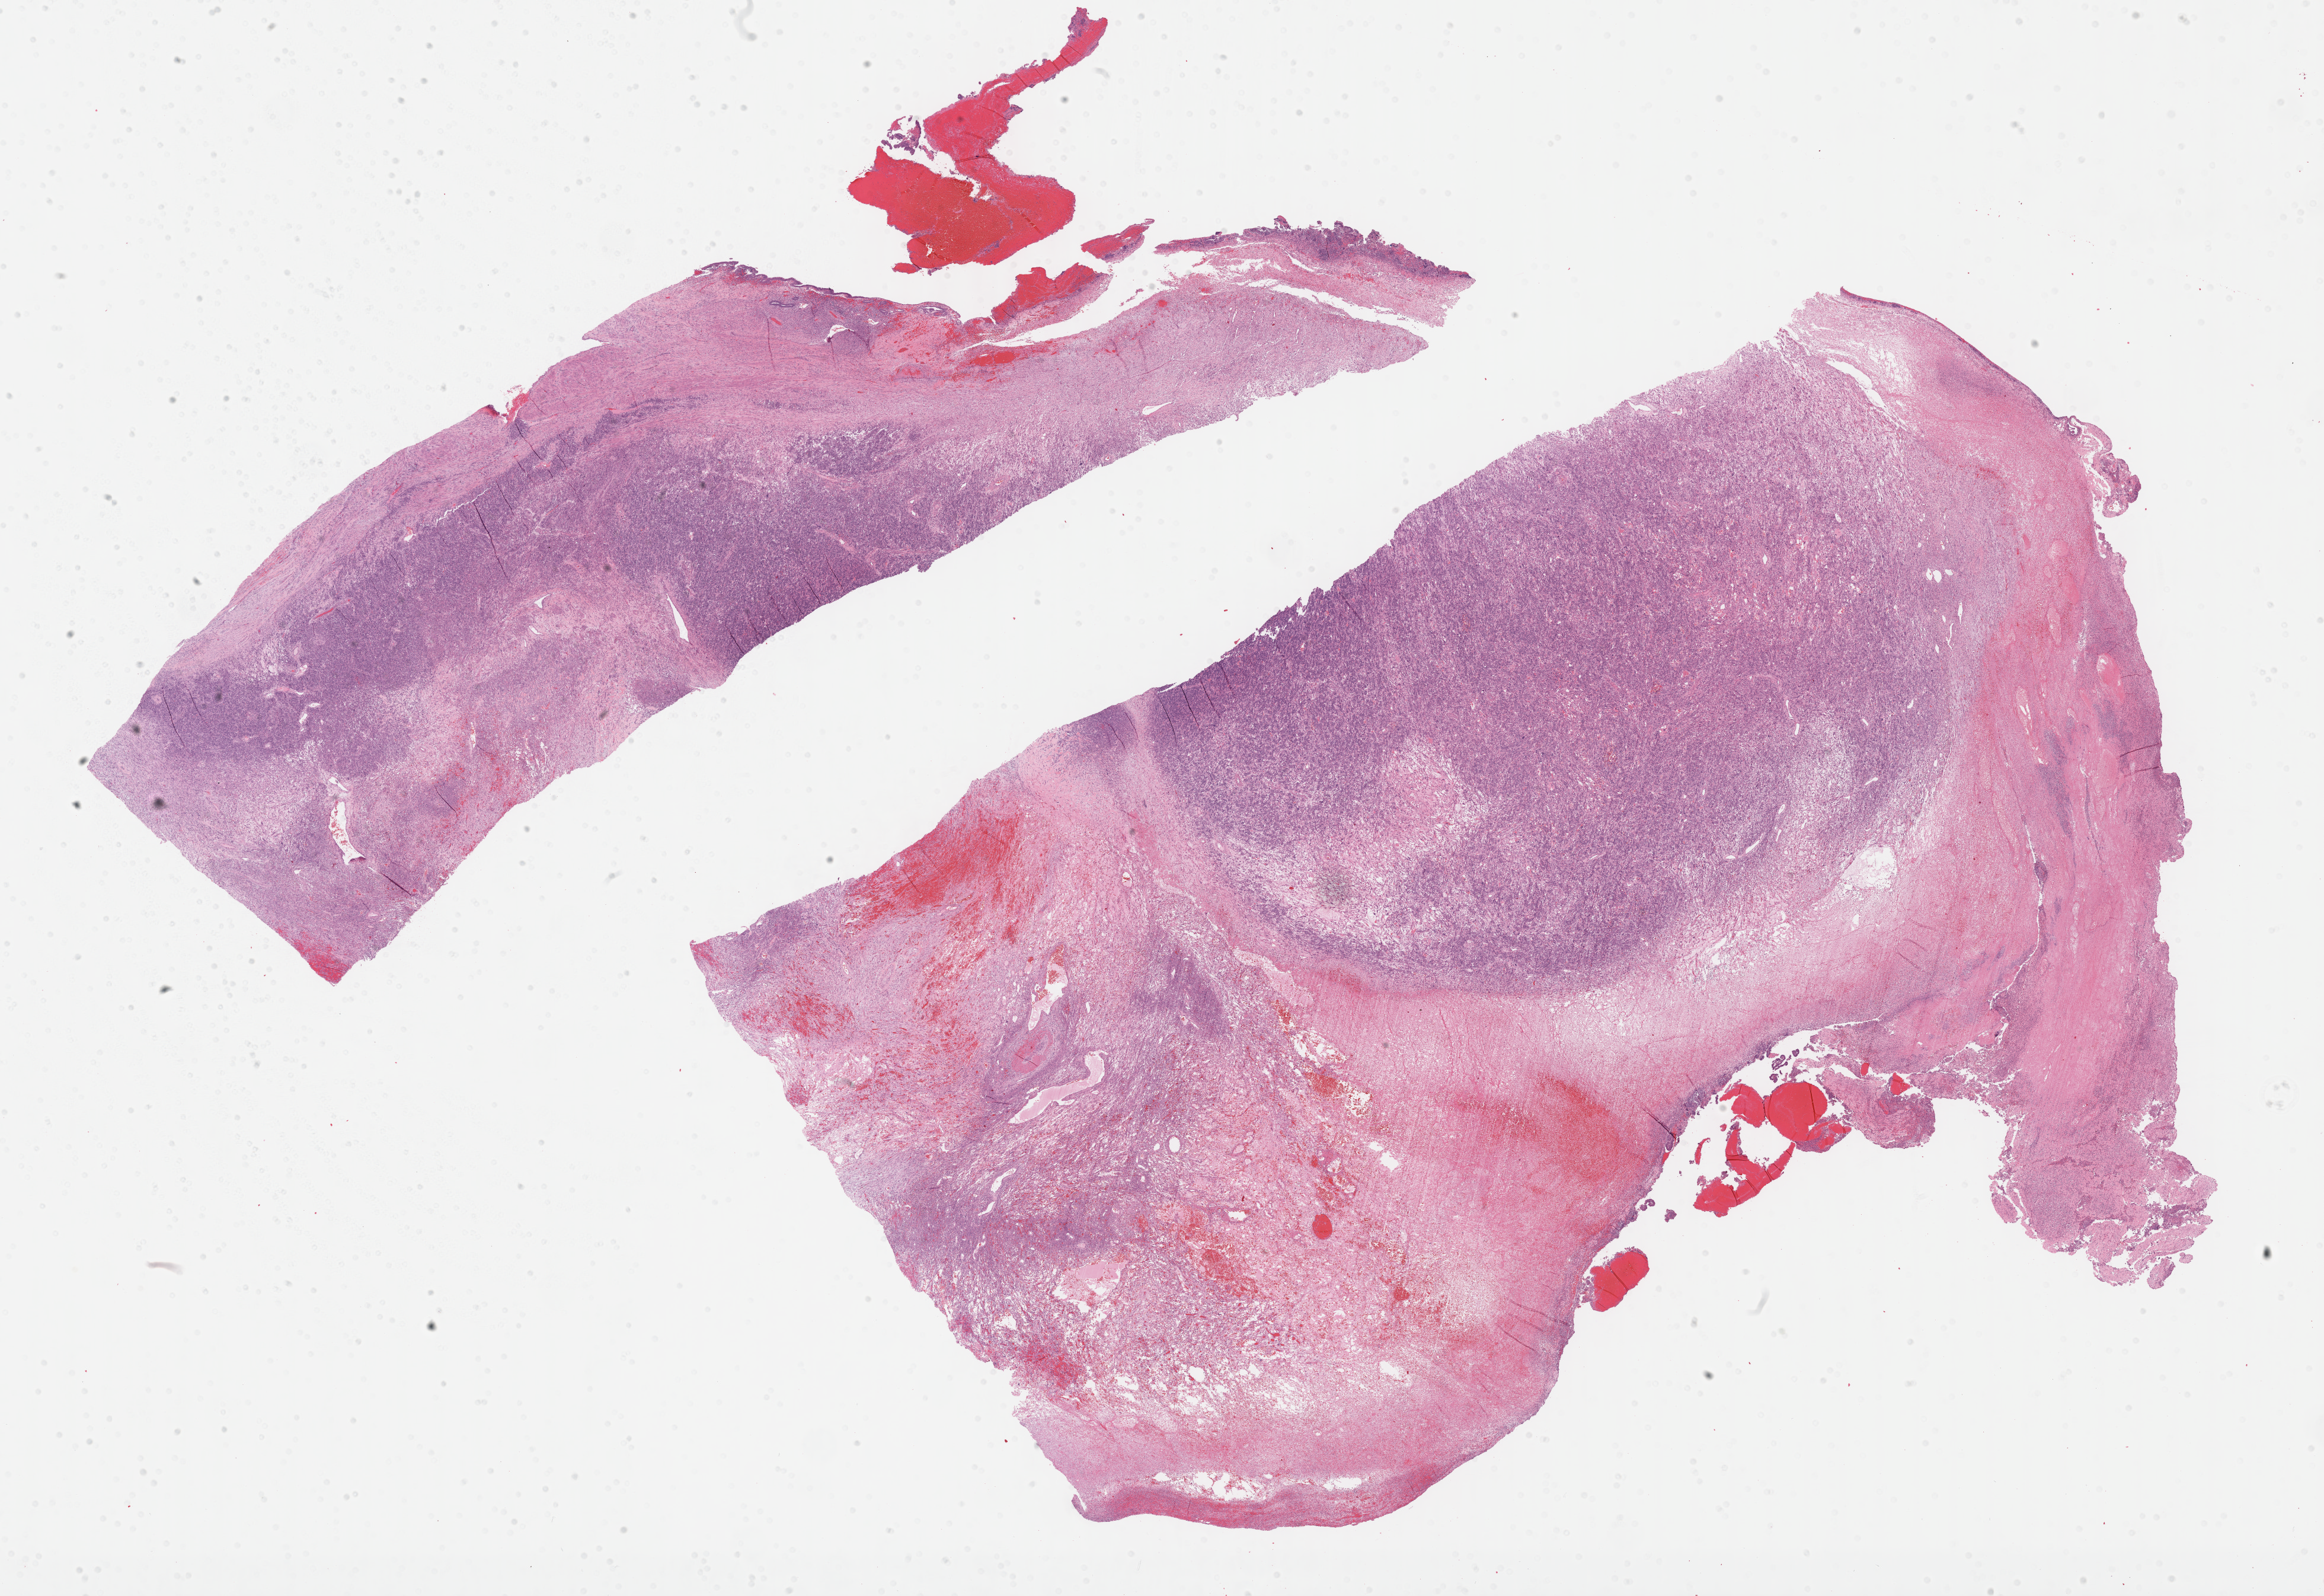
Digitized H&E tissue section (whole slide) — whole scanned area (about 31.7 x 21.8 mm, acquisition: 40x scan) shown as a low-resolution overview. Formalin-fixed paraffin-embedded (FFPE) diagnostic section. Primary tumour sample from the uterus. Female, age 49 years at initial diagnosis.
Pathologic diagnosis: Leiomyosarcoma, NOS.